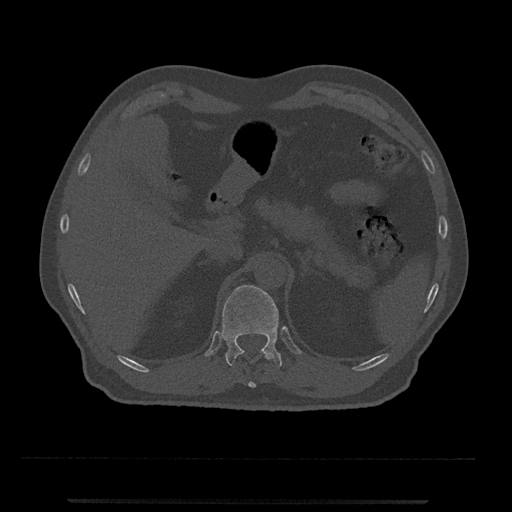
CT including the spine, one axial slice; position 421 of 797 along the scan axis; reconstruction kernel Br40s/3; bone window (W 1800 / L 400 HU); 0.5 mm slice thickness; 512 × 512 image matrix, field of view 419 × 419 mm. Patient: male, 63 years. From the clinical record (not read from this slice): primary cancer: prostate.
Annotated regions visible in this slice (semi-automatic segmentation, software-assisted and operator-edited):
- T11 vertebra: bounding box [x1, y1, x2, y2] px = [236, 350, 271, 388]
- T12 vertebra: [222, 285, 282, 367]